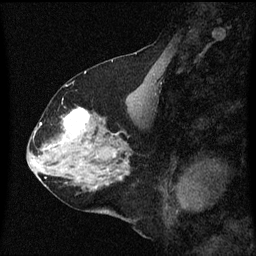
Breast MRI (dynamic contrast-enhanced), one sagittal slice; slice 26 of 60 in the series (ordered by position); dynamic contrast-enhanced series, image 2 of 3 at this slice position (ordered by acquisition); 1.5 T; TE 4.2 ms, TR 8 ms; 256 × 256 image matrix, field of view 200 × 200 mm. Female patient, age 58 years.
Annotated regions visible in this slice (semi-automatic segmentation, software-assisted and operator-edited):
- analysis volume of interest (the breast-tissue region the enhancement analysis was run in; not a lesion): bounding box (x1, y1, x2, y2) in pixels: (56, 108, 99, 149)
- tumour enhancement mask (voxels above the 70 % enhancement threshold inside the analysis volume of interest): (60, 108, 91, 145)